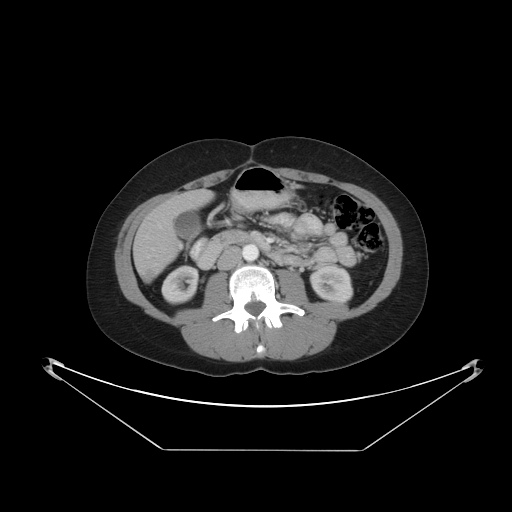
Contrast-enhanced abdominal CT, one axial slice. Slice 14 of 48 in the series (ordered by position). Reconstruction kernel STANDARD. 120 kVp. Intravenous contrast given. Soft-tissue window (W 400 / L 40 HU). 5 mm slice thickness. 512 × 512 image matrix, field of view 482 × 482 mm. Female patient, age 38 years. Case-level facts recorded for this patient, not image findings: diagnosis: colorectal cancer liver metastases, imaged before liver resection; multiple liver metastases: yes; largest metastasis: 2.5 cm; chemotherapy before resection: no.
Outlined on this slice (expert manual segmentation):
- liver: bounding box [x1, y1, x2, y2] px = [135, 191, 211, 283]
- planned liver remnant (the part of the liver to remain after resection): [170, 191, 212, 212]
- portal vein (with intrahepatic branches): [148, 256, 150, 258]
- liver metastasis: [146, 274, 155, 281]